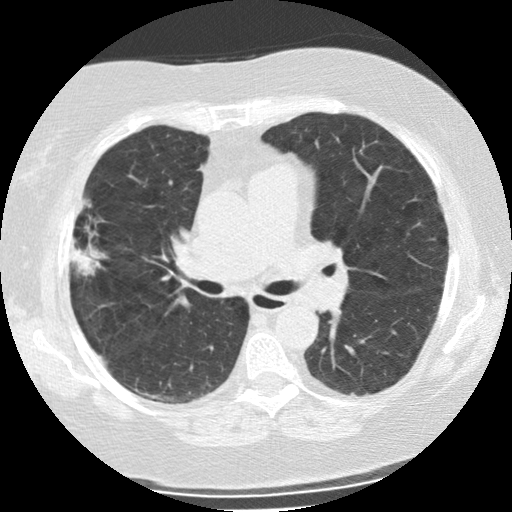
Low-dose screening chest CT, axial slice; second screening round (one year after baseline); lung window (W 1500 / L -600 HU); 2.5 mm slice thickness; standard (soft-tissue) reconstruction kernel (STANDARD). Female, age 73 years at enrolment. Former smoker at enrolment.
Expert reader's lesion annotation, box from (x=56, y=205) to (x=107, y=279) px. The screening reader recorded 2 non-calcified nodules or masses ≥4 mm on this exam (right upper lobe, left upper lobe); which of them this box marks is not recorded. Lung cancer was diagnosed 47 days after this screen: bronchiolo-alveolar adenocarcinoma, NOS, right upper lobe, moderately differentiated (G2), stage IIIB (AJCC 6th edition), 21 mm at pathology.